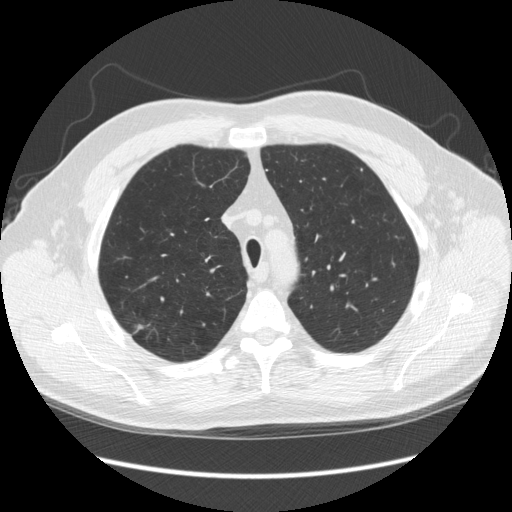
Low-dose screening chest CT, one axial slice. Slice 194 of 248 in the series (ordered by position). Lung window (W 1500 / L -600 HU). 2.5 mm slice thickness. 512 × 512 image matrix.
Outlined on this slice (manually delineated by an expert):
- lesion 1 (tumor, upper lobe of right lung): bounding box (x1, y1, x2, y2) in pixels: (137, 323, 144, 330)